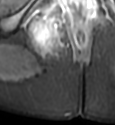
MRI of an extremity soft-tissue mass, one axial slice. Position 32 of 49 along the scan axis. STIR. MR volume resampled by the dataset authors to the PET/CT grid (not the native acquisition matrix). 3.27 mm slice thickness. 115 × 125 image matrix, field of view 112 × 122 mm. Female patient. Case-level facts recorded for this patient, not image findings: histological type: epithelioid sarcoma; grade: intermediate; site of the primary tumour: right buttock.
Outlined on this slice (expert contour drawn on MRI and transferred to this co-registered scan by the dataset authors):
- gross tumour volume including surrounding oedema: box from (x=29, y=14) to (x=64, y=56) px
- gross tumour volume (mass): (x=31, y=21)–(x=55, y=47)